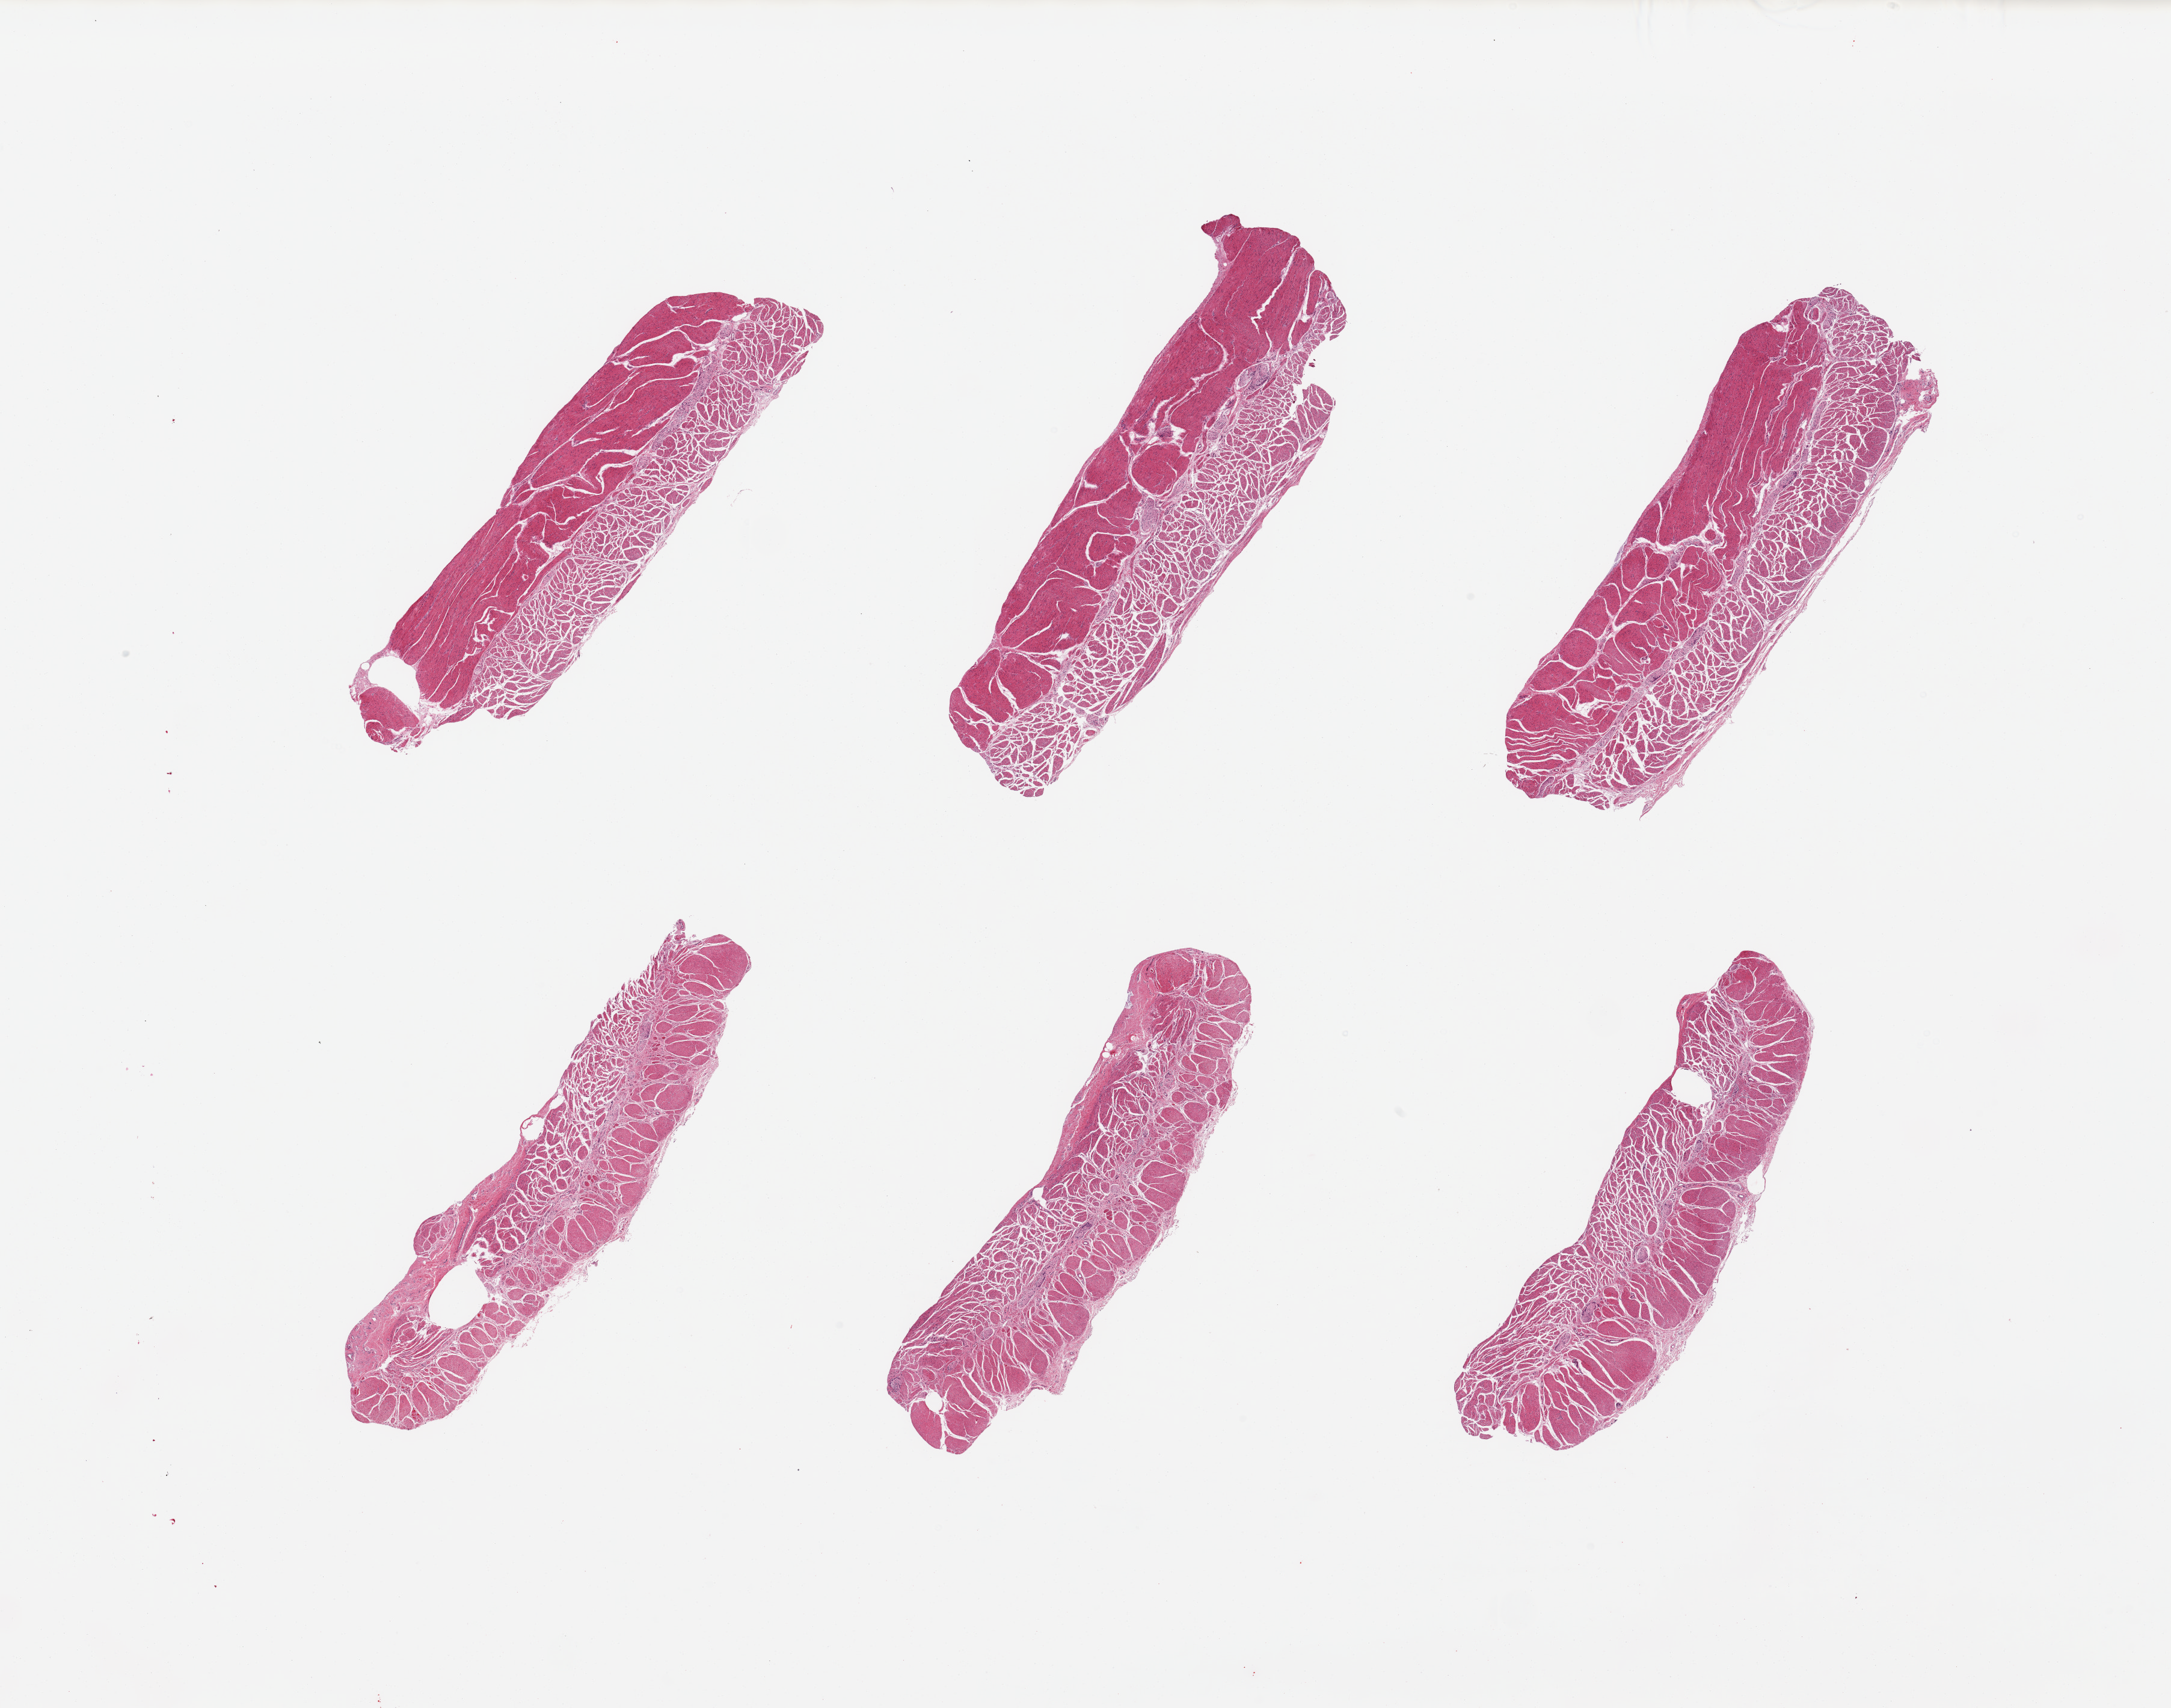
Whole-slide image, hematoxylin and eosin (H&E) stain — whole scanned area (about 28.5 x 22.5 mm, from a 20x scan) shown as a low-resolution overview; PAXgene-fixed paraffin-embedded (PFPE) section; section of esophageal muscle (target tissue); tissue donor sample. Female donor.
Review note (as recorded): 6 pieces; well trimmed target muscularis.